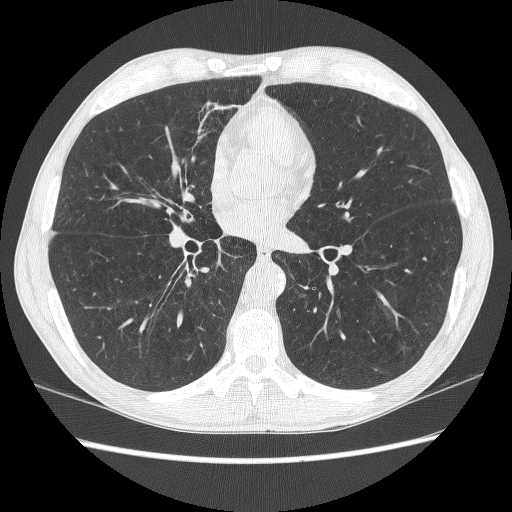
Chest CT (low-dose screening protocol), one axial image; baseline screening round; lung window (W 1500 / L -600 HU); 1.25 mm slice thickness; lung (sharp) reconstruction kernel (BONE); 512 × 512 image matrix, field of view 353 × 353 mm. Male participant, aged 62 years at enrolment.
- Lesion marked by an expert reader, bounding box <328,200,365,230> (left, top, right, bottom; pixels).
- Reader record for this screening exam (exam-level; its link to the box is not recorded): non-calcified nodule or mass ≥4 mm, right lower lobe, 8 × 4 mm, poorly defined margins, soft tissue attenuation, pre-existing on the prior screen: no.
- Note: the box lies in the patient's left hemithorax on this image, whereas the reader's record names the right lung; they may be different findings.
- Lung cancer was diagnosed 452 days after this screen (after the second annual screen): small cell carcinoma, NOS, left upper lobe, stage IIIA (AJCC 6th edition).